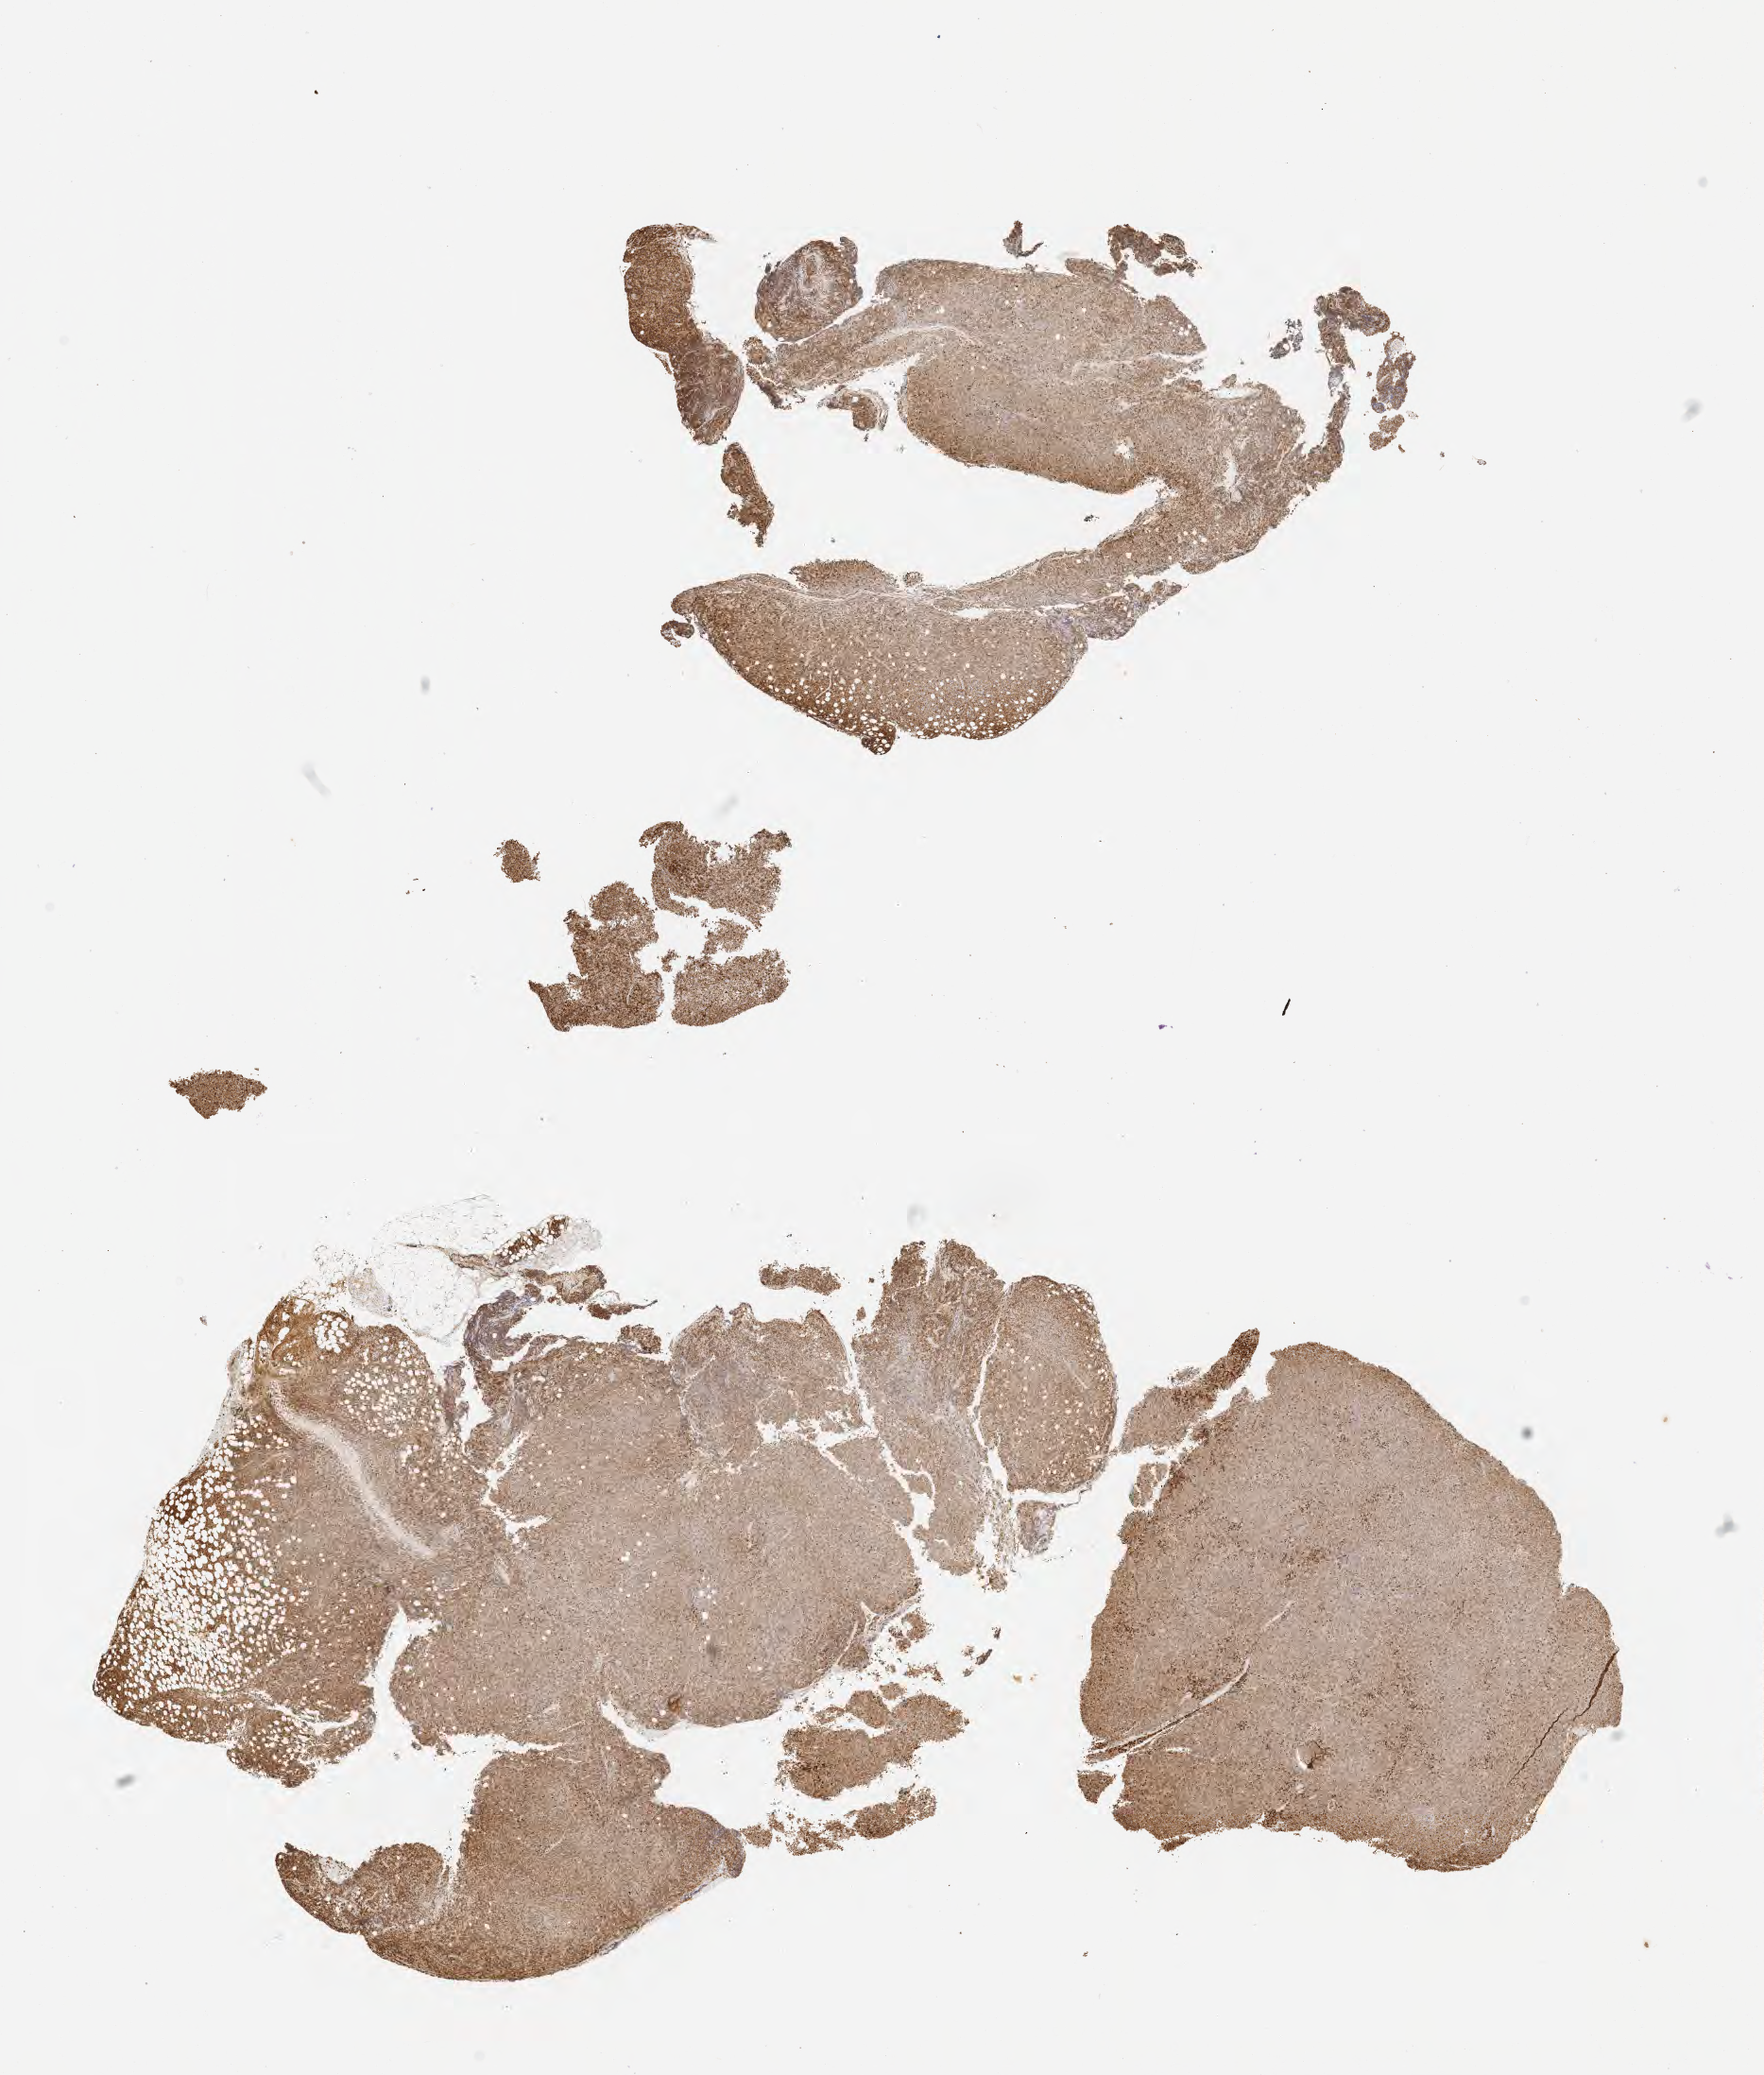
Whole-slide image, immunohistochemical stain for CD79a, a low-resolution overview of the entire scanned area, about 15.1 x 17.7 mm, tumor tissue. Patient: female, age 32 years.
Diagnosis: Diffuse large B-cell lymphoma, NOS.